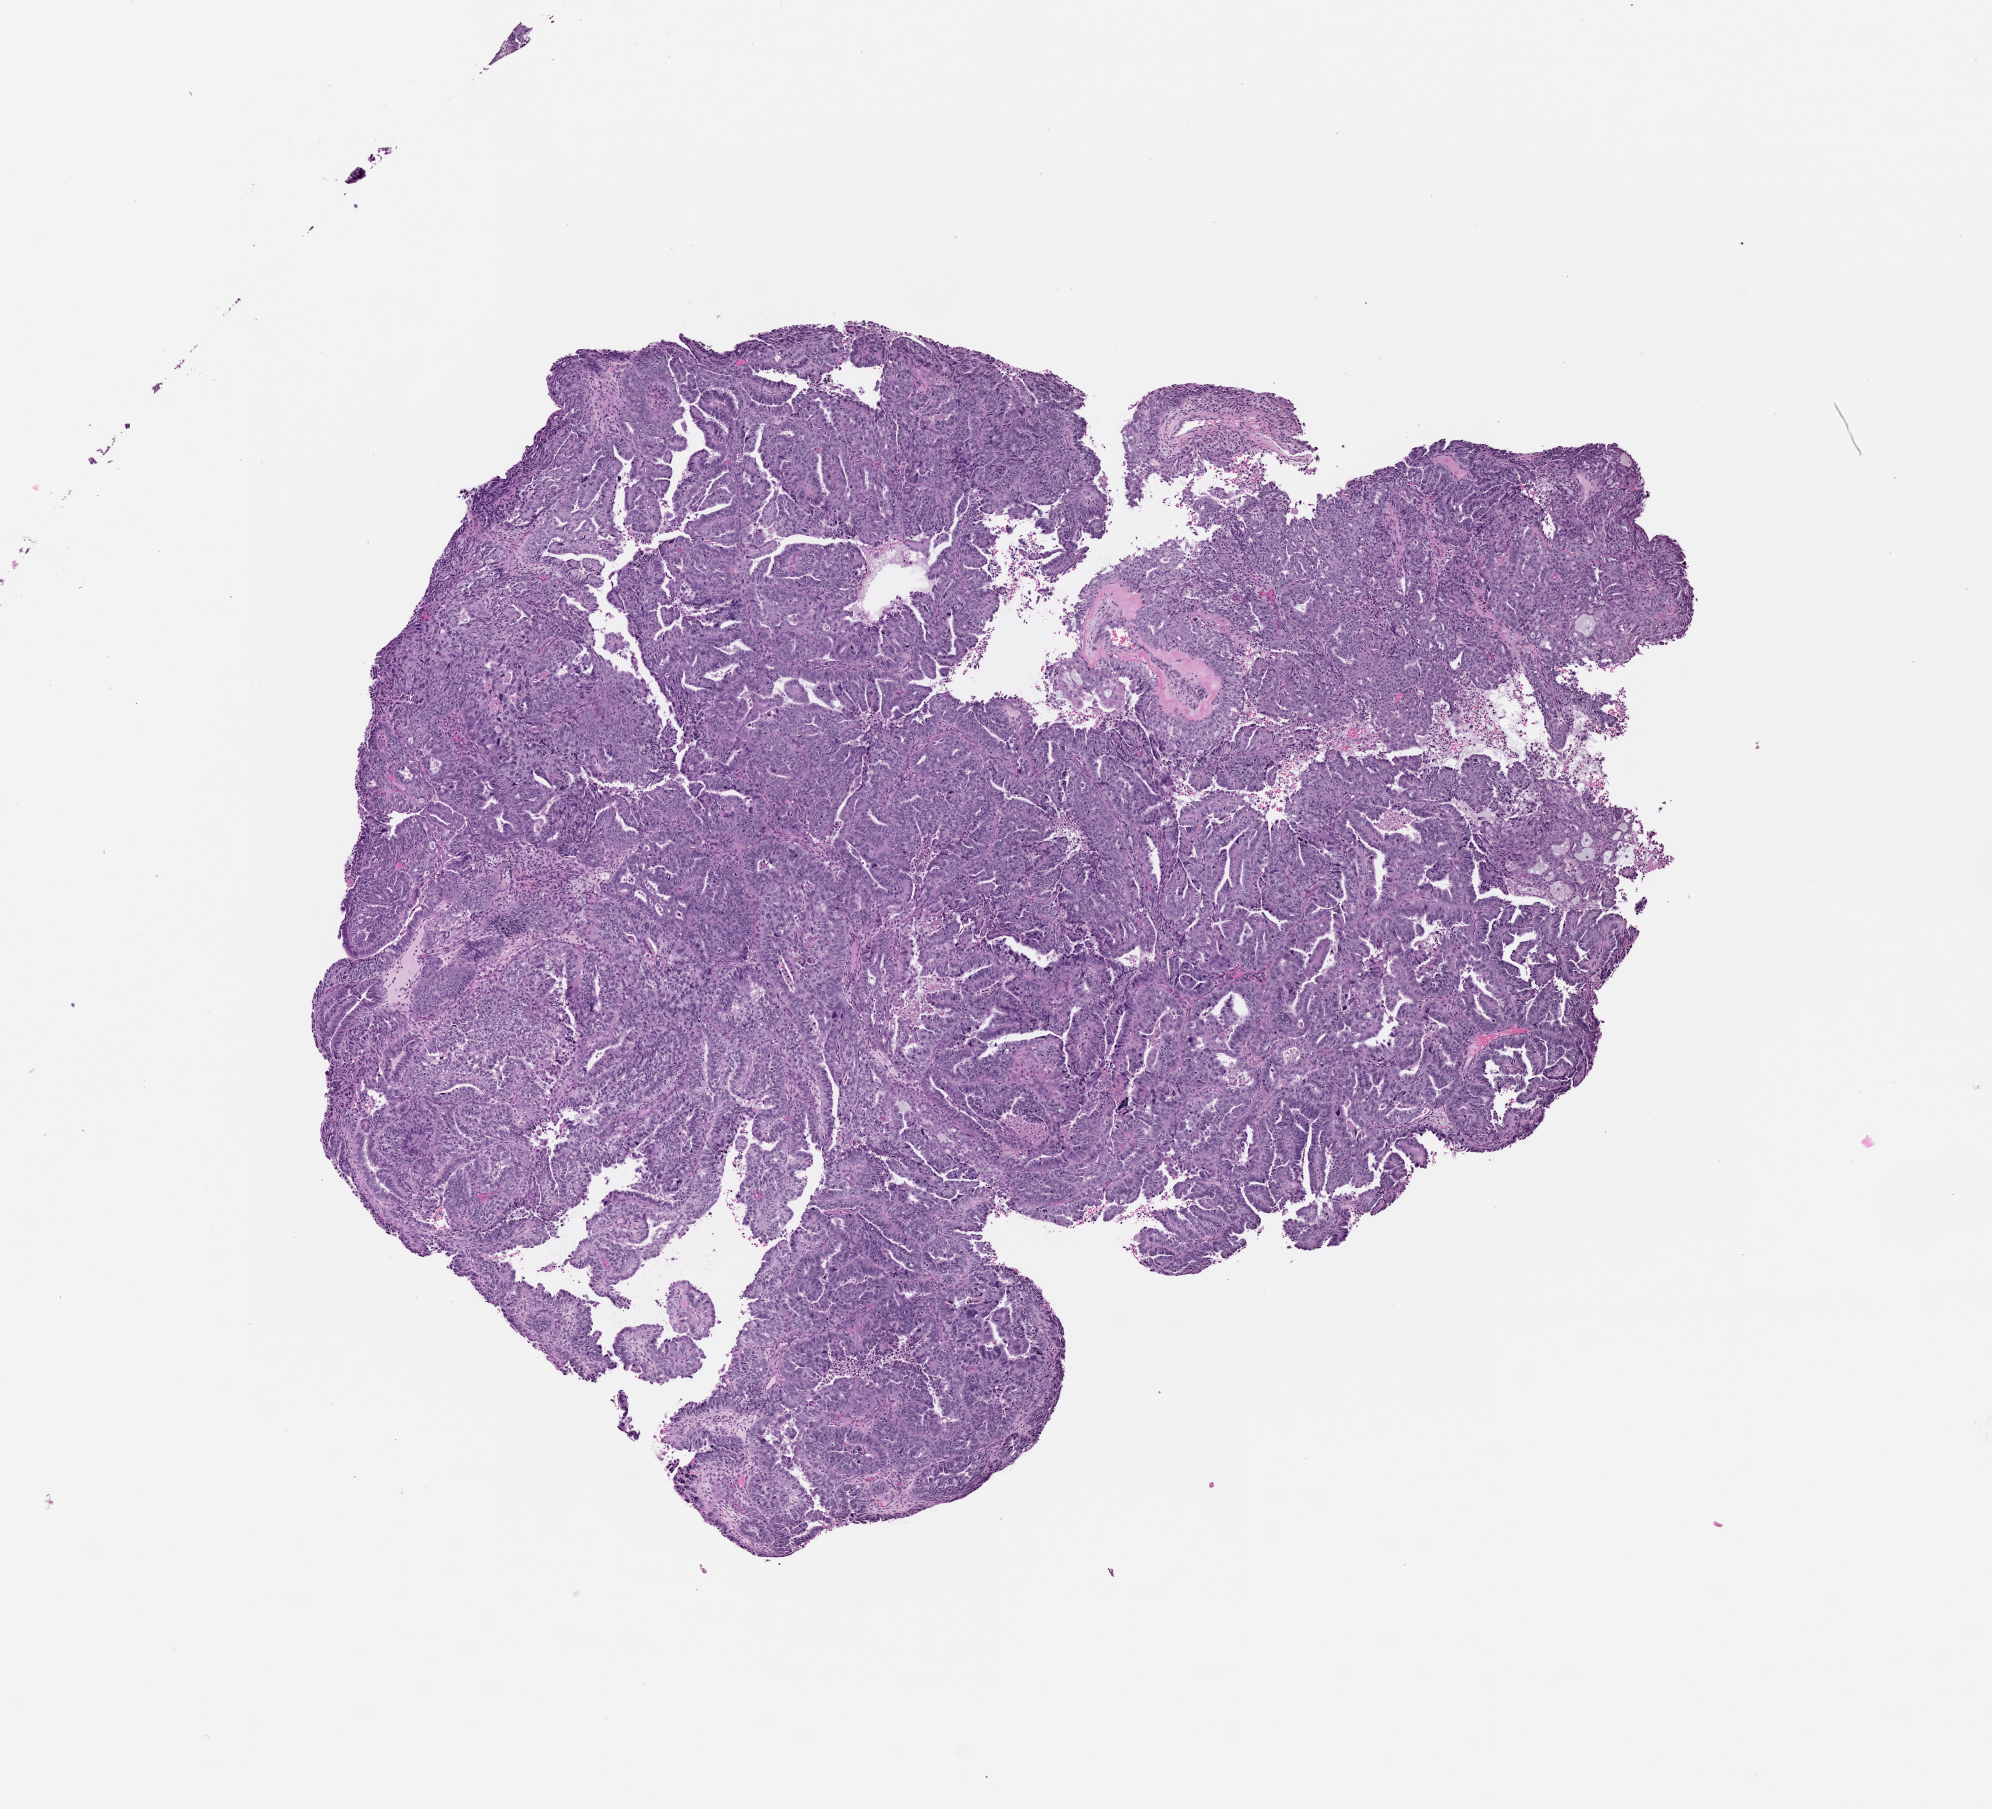
Whole-slide histology image, H&E — a low-resolution overview of the entire scanned area, about 8.0 x 7.3 mm (slide scanned at 20x); uterus, tumour tissue. Female, 58 y/o. Histologic grade: G3 (poorly differentiated).
Primary tumour site (as recorded): posterior endometrium. AJCC pathologic stage: IIIC1. Histologic diagnosis: Endometrioid adenocarcinoma, NOS.